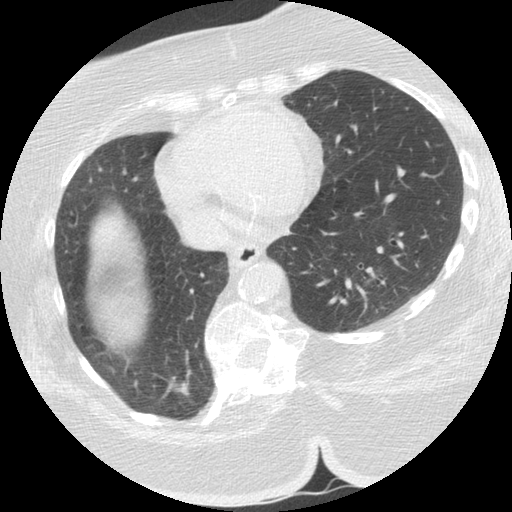
Low-dose screening chest CT, one axial slice; slice 53 of 151 in the series (ordered by position); 140 kVp; lung window (W 1500 / L -600 HU); 2.5 mm slice thickness; 512 × 512 image matrix, field of view 340 × 340 mm.
Structures marked on this image (expert manual segmentation):
- lesion 1 (tumor, lower lobe of right lung): box from (x=175, y=376) to (x=190, y=396) px